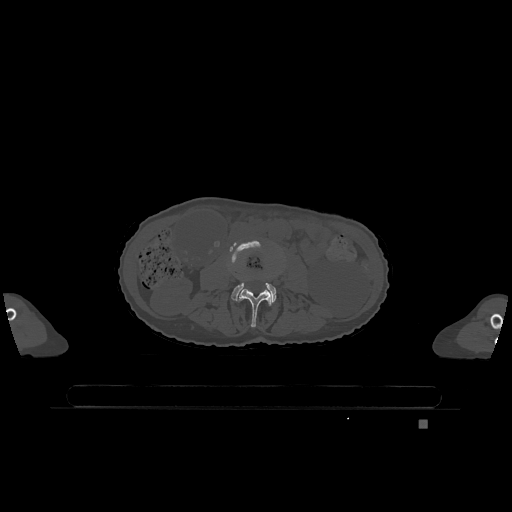
CT including the spine, one axial slice. Slice 337 of 1317 in the series (ordered by position). Bone window (W 1800 / L 400 HU). 512 × 512 image matrix, field of view 500 × 500 mm. Patient: female, 74 years. Case-level facts recorded for this patient, not image findings: primary cancer: lung.
Annotated regions visible in this slice (semi-automatic segmentation, software-assisted and operator-edited):
- L3 vertebra: box from (x=238, y=289) to (x=272, y=327) px
- L4 vertebra: (x=230, y=241)–(x=277, y=303)